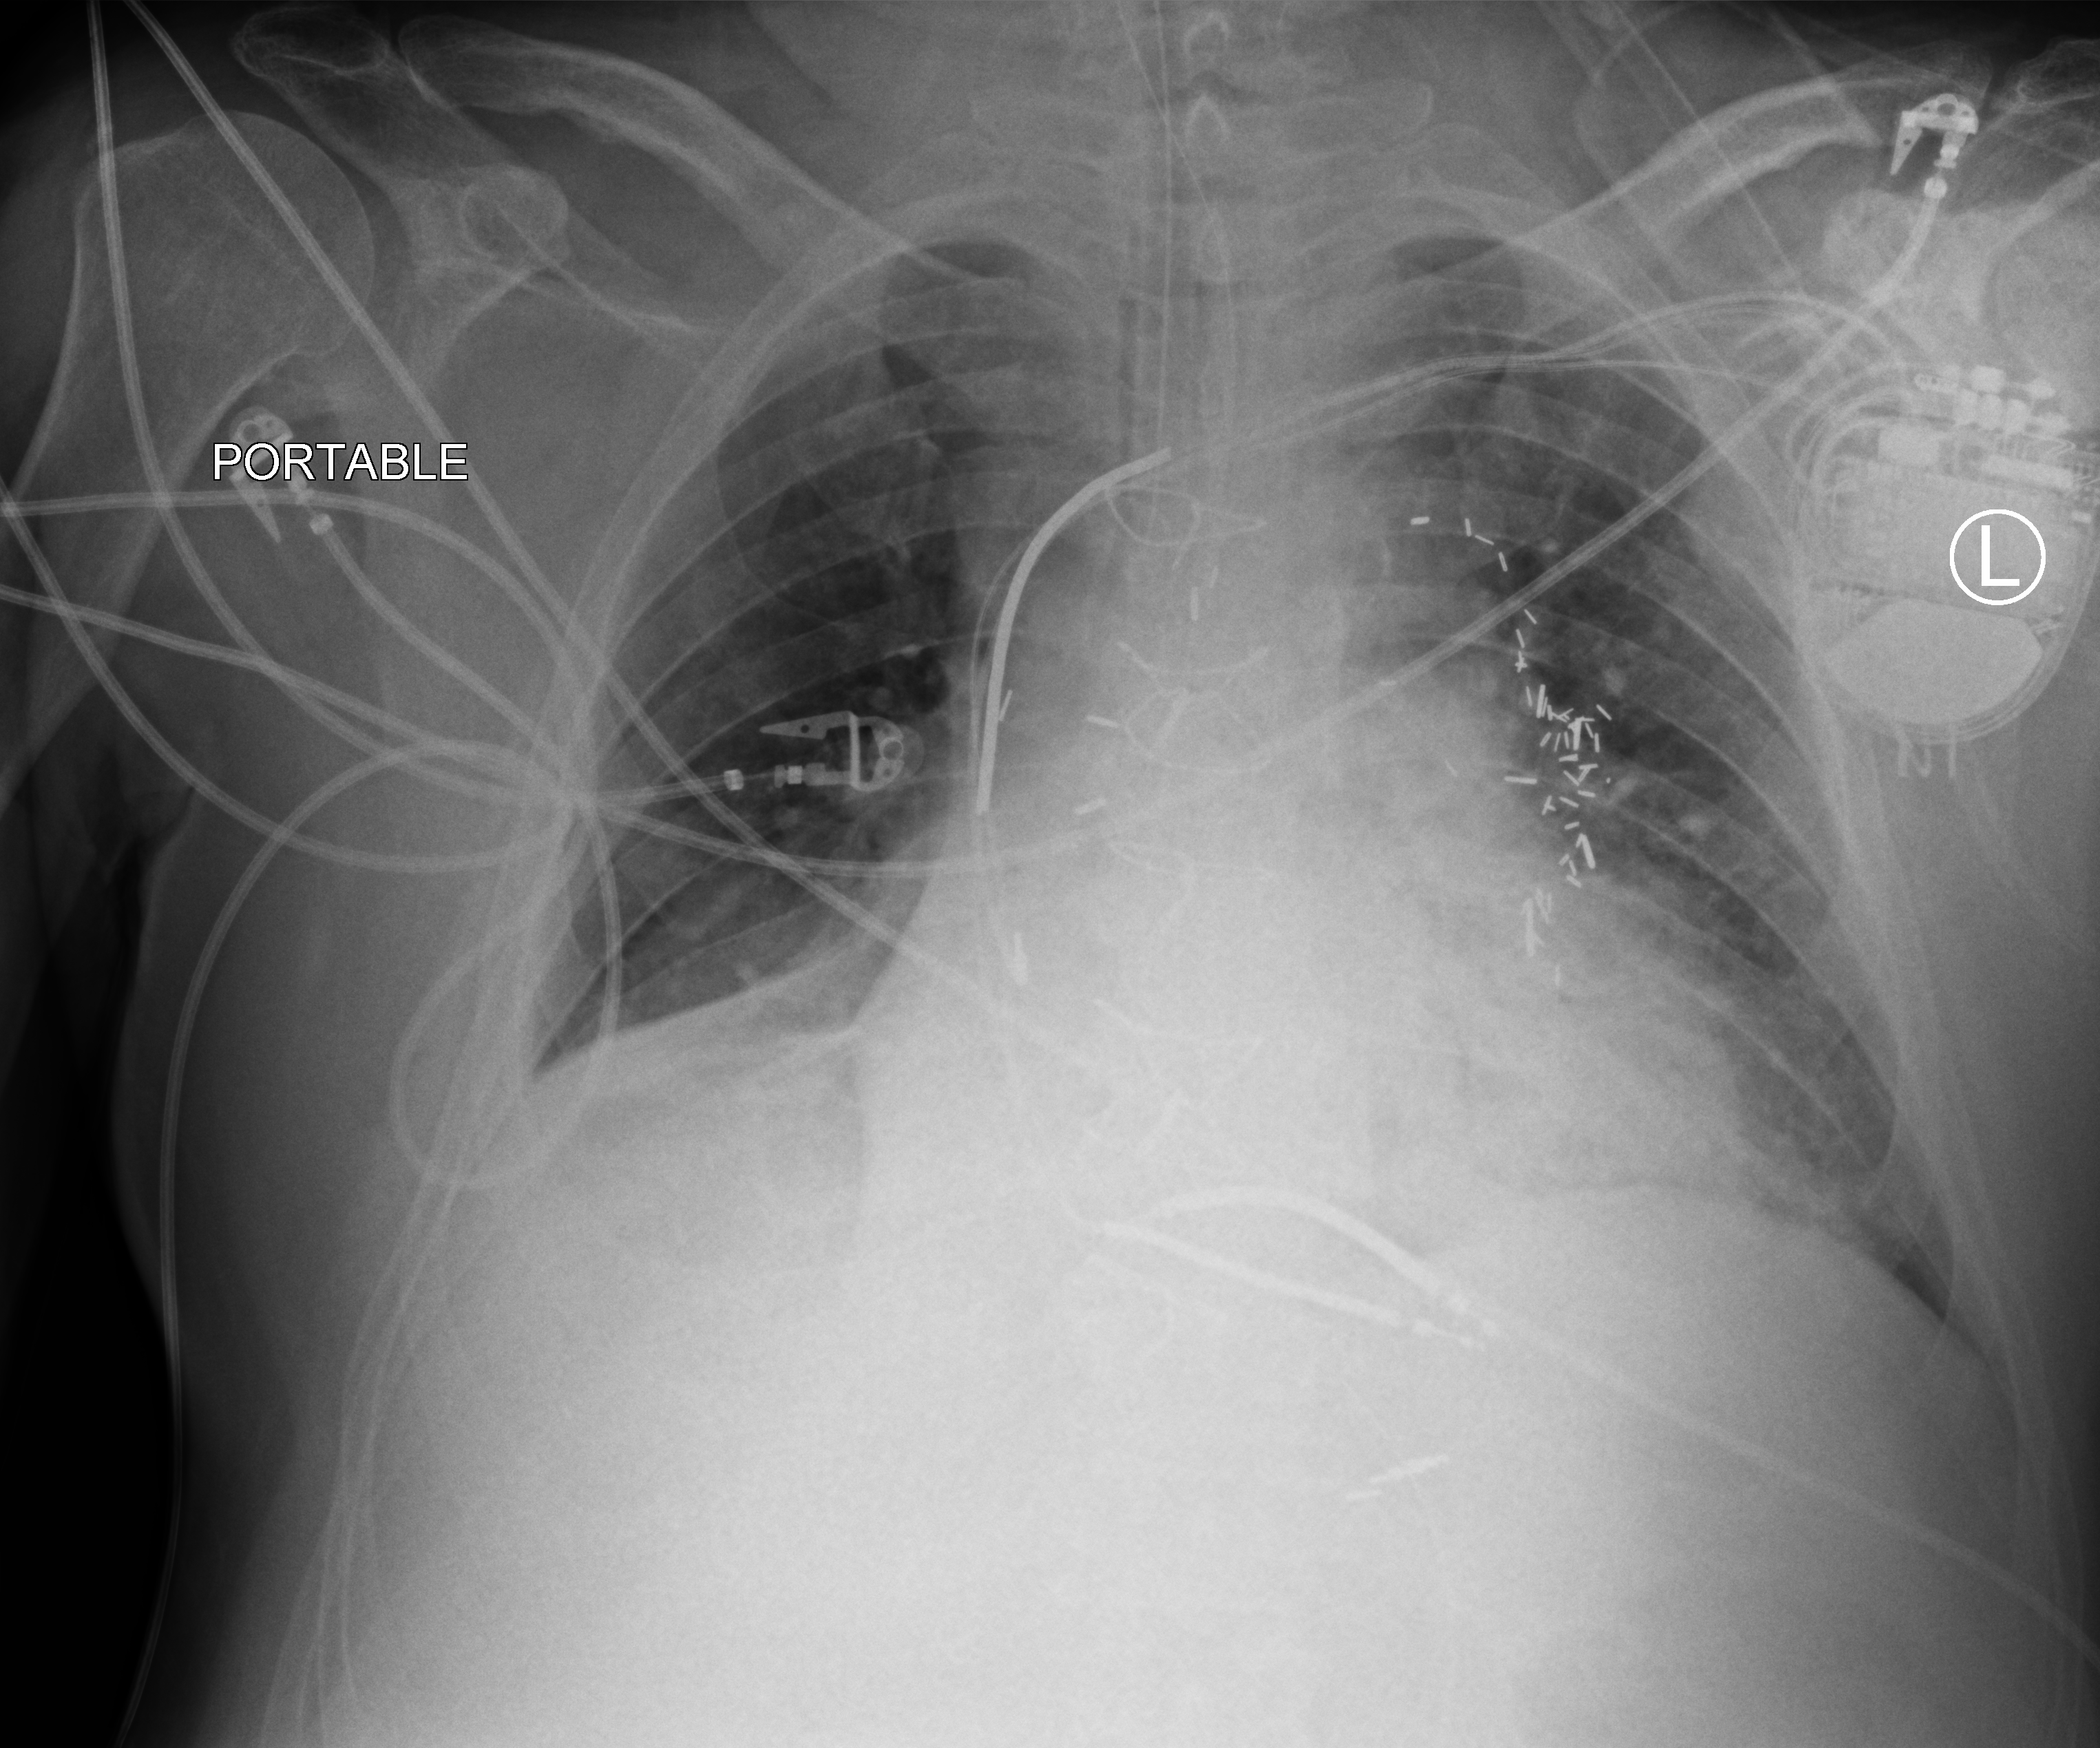
Bedside chest radiograph (computed radiography); anteroposterior (AP) projection. Male patient hospitalised with COVID-19, age 60–74 years.
Admission-level facts for this patient (not findings on this image; timing relative to this image not recorded): length of hospital stay: 55 days; hypertension (admission record): yes; admitted to intensive care during this hospital stay: yes.